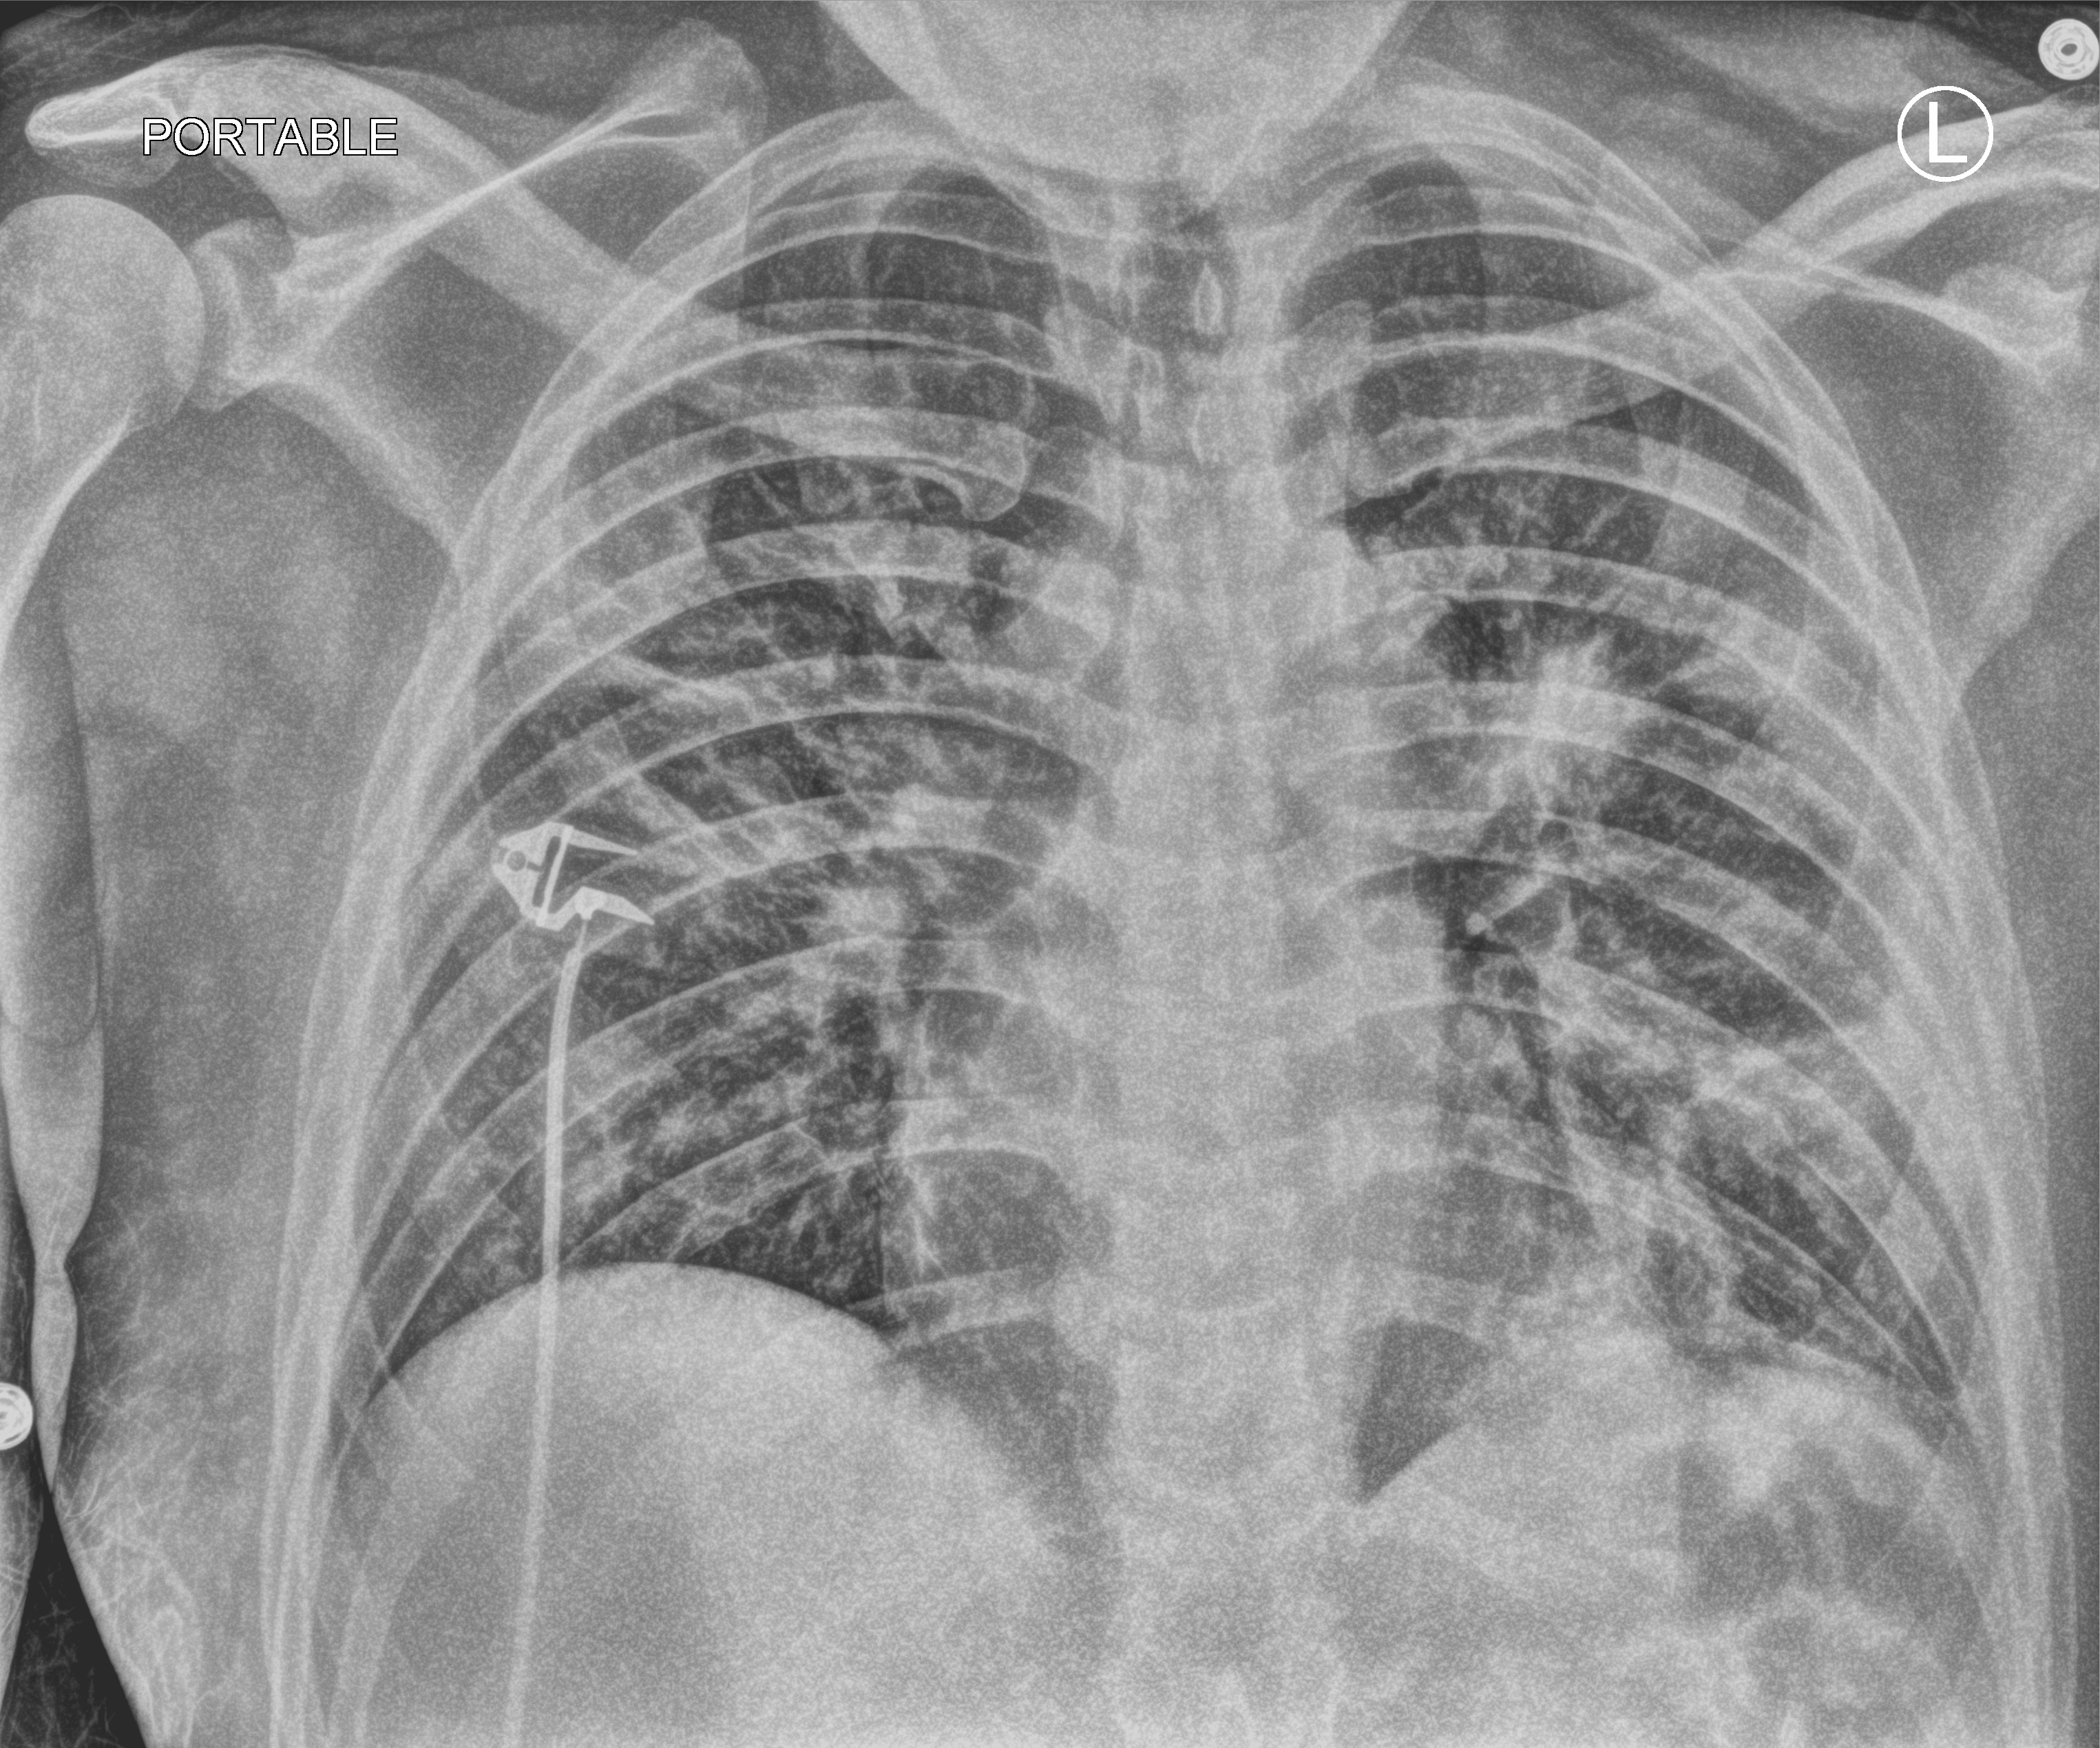
Portable chest radiograph; anteroposterior (AP) projection. Male patient hospitalised with COVID-19, age 18–59 years.
From the hospital-stay record, not from the radiograph (when in the stay this image was taken is not recorded):
- hypertension (admission record): no